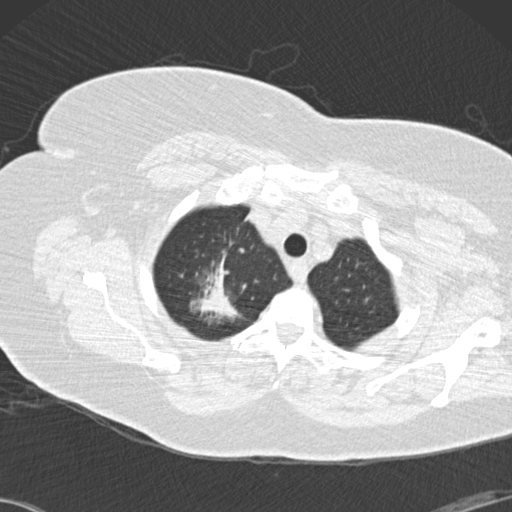
Low-dose screening chest CT, one axial slice. Position 126 of 146 along the scan axis. 120 kVp. Lung window (W 1500 / L -600 HU). 2 mm slice thickness. 512 × 512 image matrix, field of view 350 × 350 mm.
Annotated regions visible in this slice (manually delineated by an expert):
- lesion 1 (tumor, upper lobe of right lung): box from (x=190, y=253) to (x=240, y=317) px